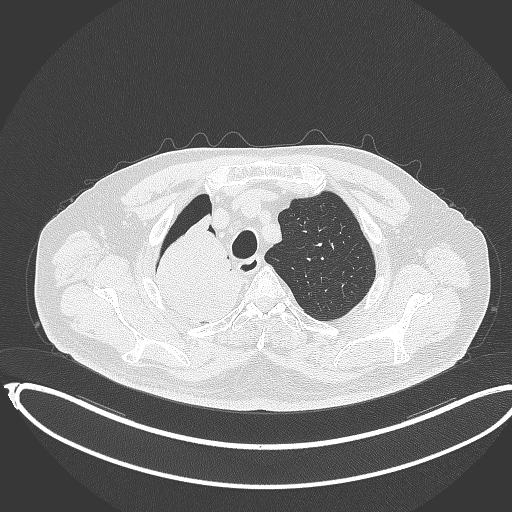
Chest CT, one axial slice. Slice 306 of 403 in the series (ordered by position). 120 kVp. Lung window (W 1500 / L -600 HU). 1 mm slice thickness. 512 × 512 image matrix, field of view 436 × 436 mm. Patient: male, 68 years. From the clinical record (not read from this slice): clinical TNM (as recorded): T2a N0 M0.
Structures marked on this image (bounding box drawn by a radiologist):
- lung tumour (recorded histology: adenocarcinoma): bounding box [x1, y1, x2, y2] px = [137, 211, 255, 328]